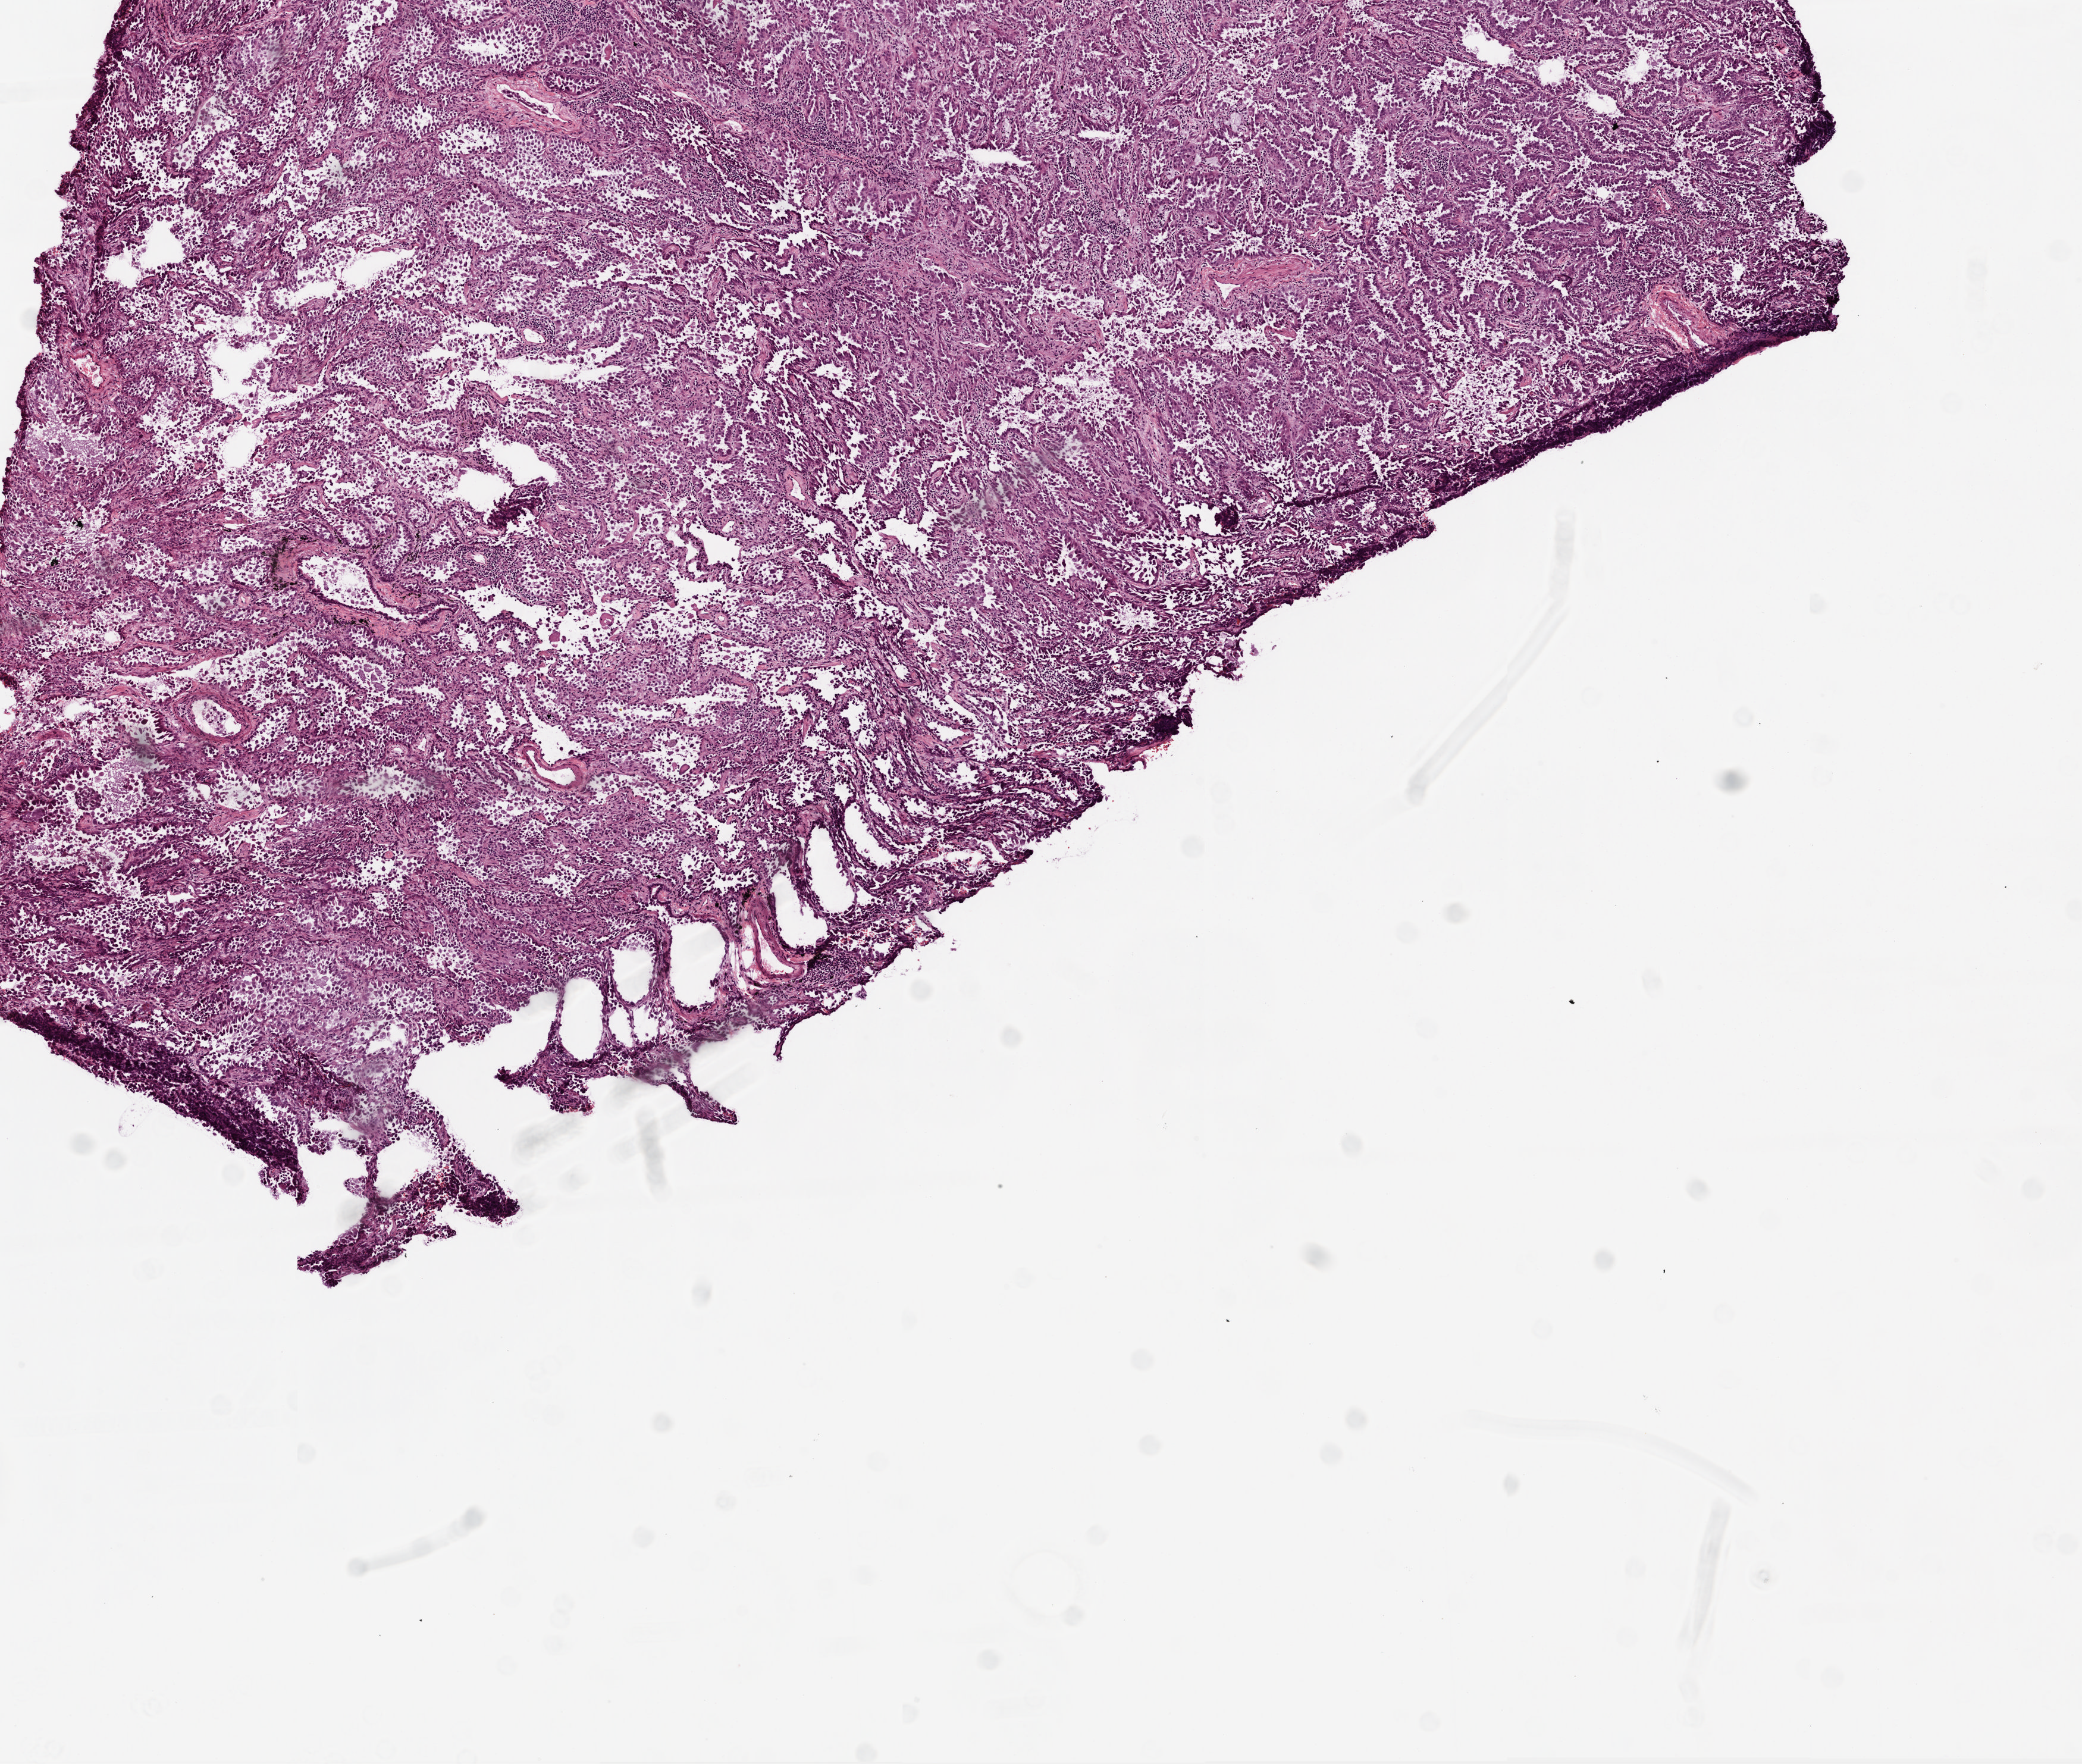
H&E-stained whole-slide image, a low-resolution overview of the entire scanned area, about 7.0 x 5.9 mm. Frozen section from the top of the tissue portion. Sample: primary tumour, lung. Female, age 65 years at initial diagnosis. Pathologist review of this section (percent, as recorded): tumour cells 80%, tumour nuclei 90%, normal cells 0%, stromal cells 20%, necrosis 0%.
Histologic diagnosis: Adenocarcinoma, NOS (upper lobe, lung). AJCC pathologic stage: IA (6th edition).